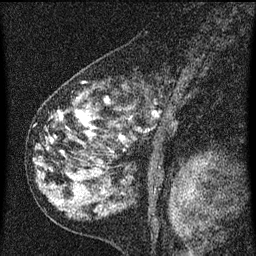
Breast MRI (dynamic contrast-enhanced), one sagittal slice; slice 37 of 60 in the series (ordered by position); dynamic contrast-enhanced series, image 2 of 3 at this slice position (ordered by acquisition); 1.5 T; TE 4.2 ms, TR 8 ms; 2 mm slice thickness; 256 × 256 image matrix, field of view 180 × 180 mm. Female patient, age 55 years.
Outlined on this slice (semi-automatically segmented with operator editing):
- analysis volume of interest (the breast-tissue region the enhancement analysis was run in; not a lesion): bounding box [x1, y1, x2, y2] px = [42, 72, 185, 155]
- tumour enhancement mask (voxels above the 70 % enhancement threshold inside the analysis volume of interest): [59, 98, 124, 141]